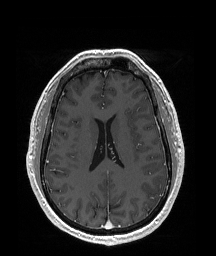
Brain MRI from a brain-tumour surgery series, one axial slice. T1-weighted post-contrast. 216 × 256 image matrix. From the clinical record (not read from this slice): histopathology: Glioblastoma; WHO grade: 4; IDH mutation: no; tumour location: Left Temporal Parietal.
Outlined on this slice (outlined manually by an expert reader):
- tumour: box from (x=142, y=179) to (x=164, y=209) px